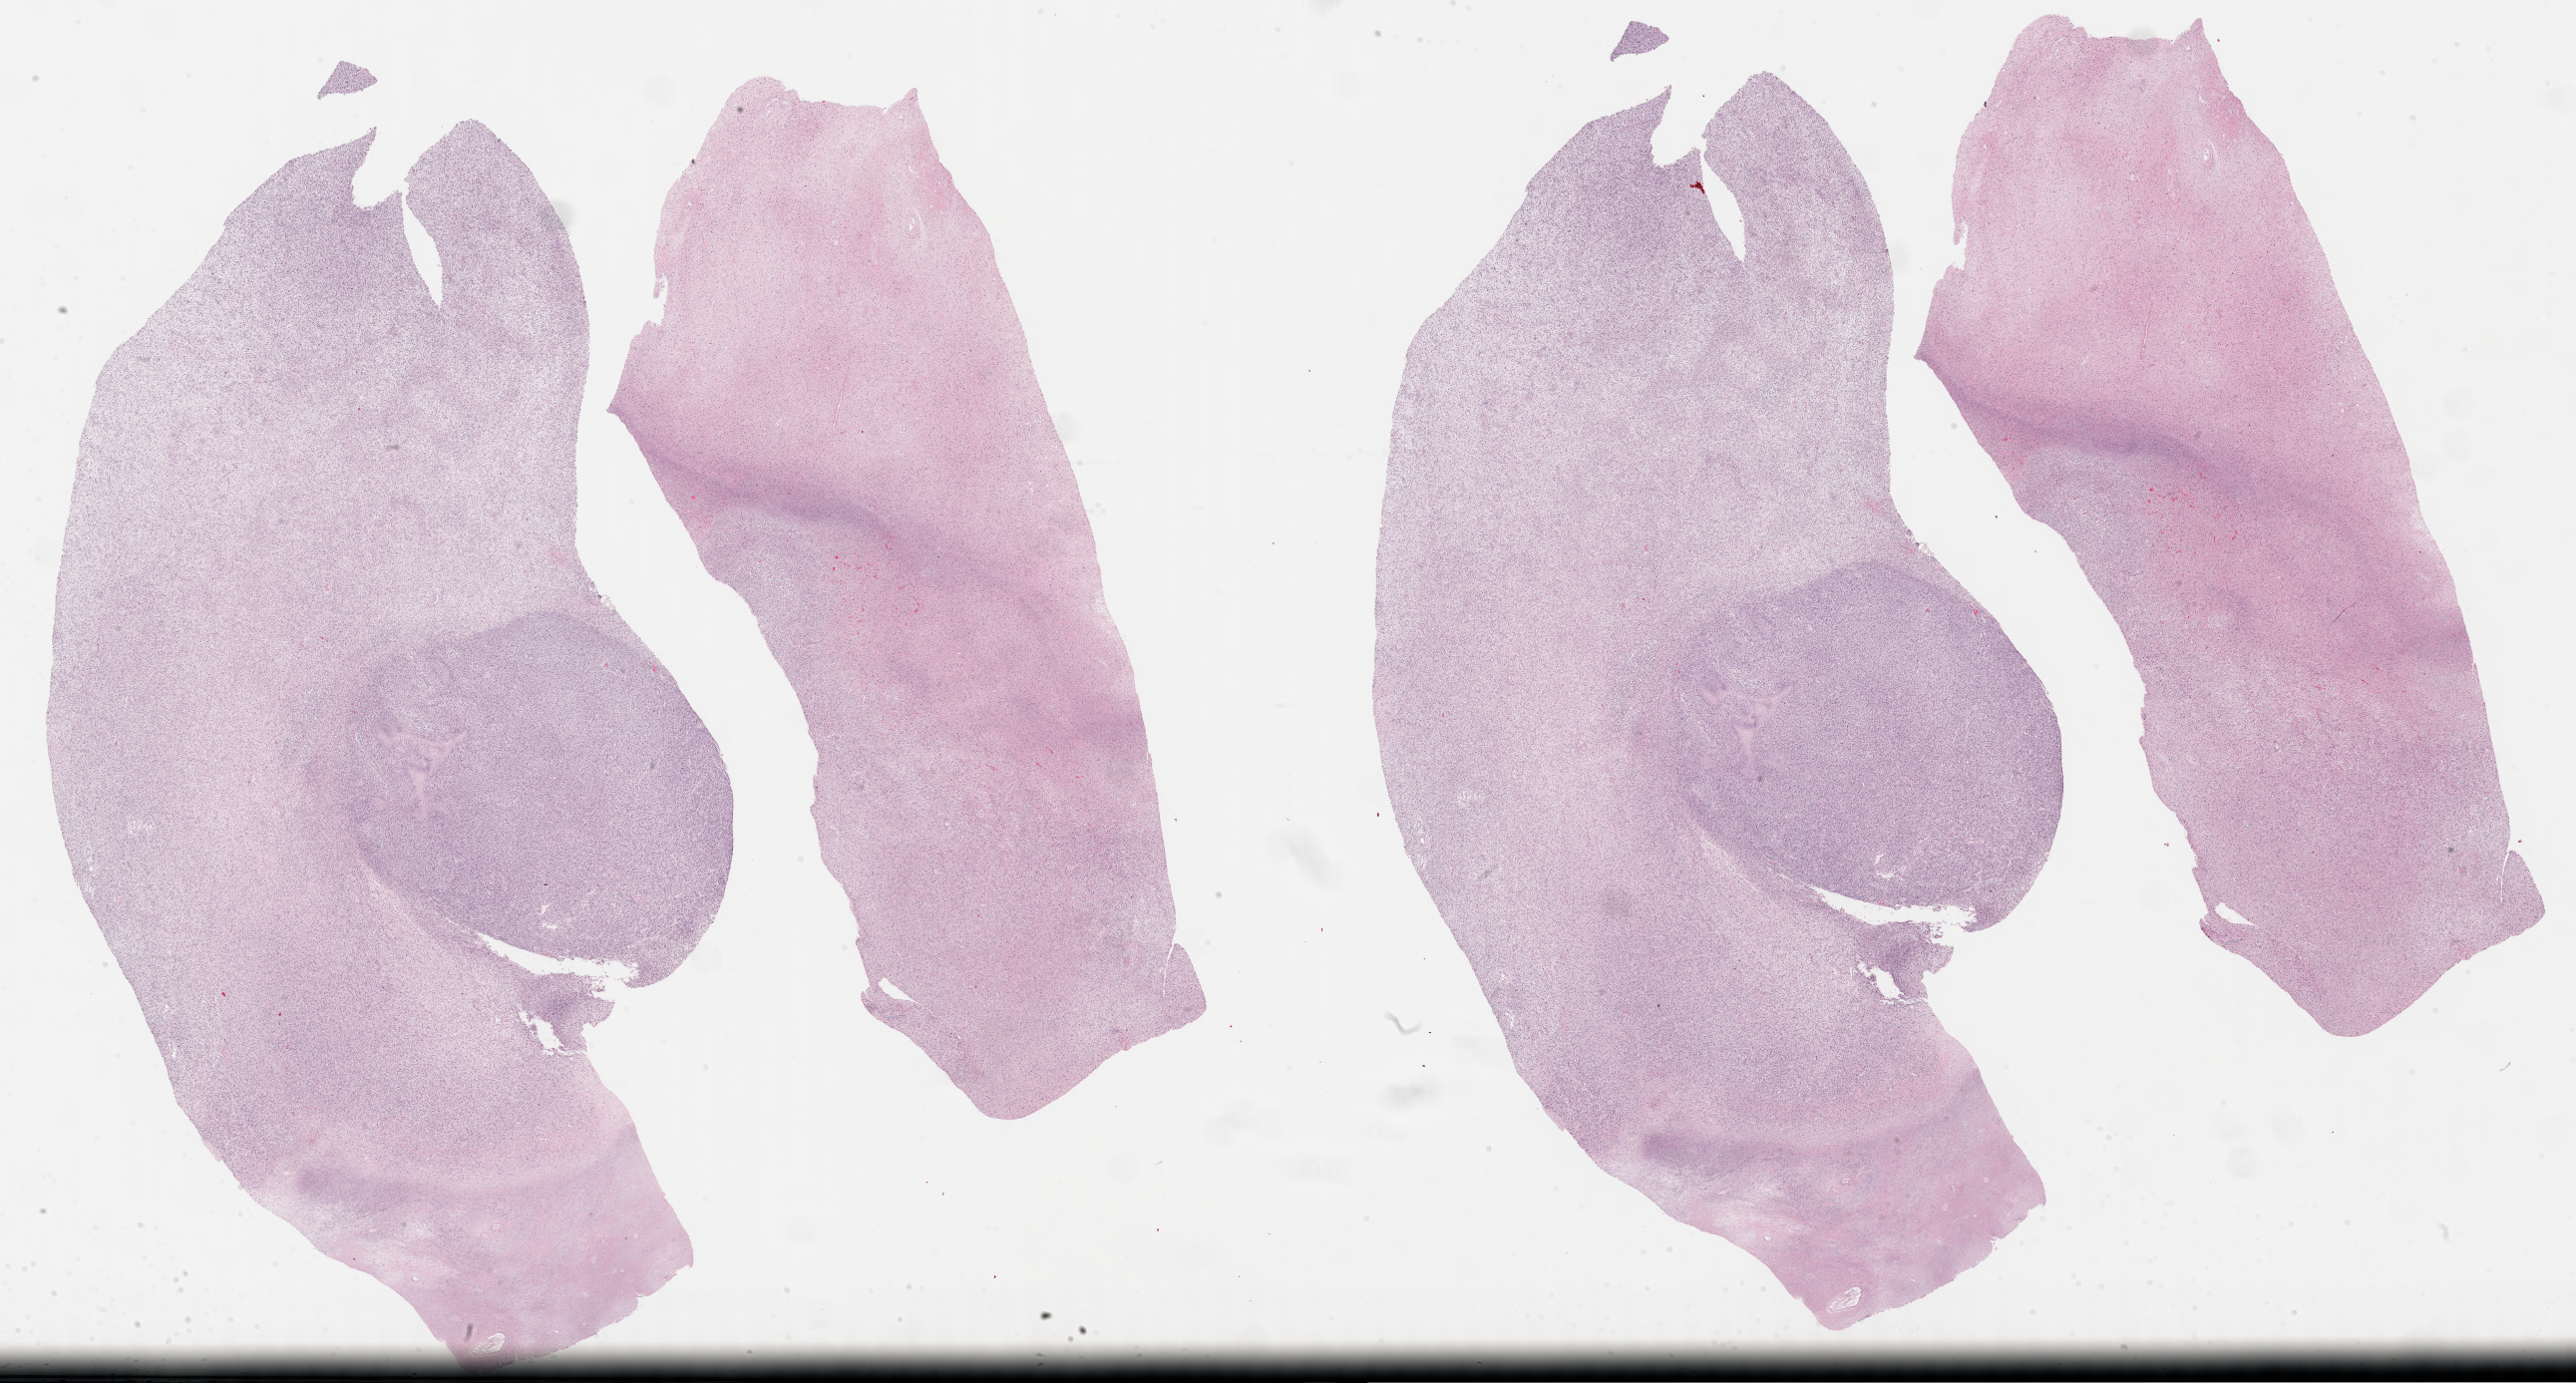
Digitized H&E-stained tissue section (whole slide), shown as a low-resolution overview of the whole scanned area (about 41.8 x 22.4 mm). Formalin-fixed paraffin-embedded (FFPE) diagnostic section. Retroperitoneum and peritoneum, primary tumour sample. Female, age 76 years at initial diagnosis.
• pathologic diagnosis: Dedifferentiated liposarcoma